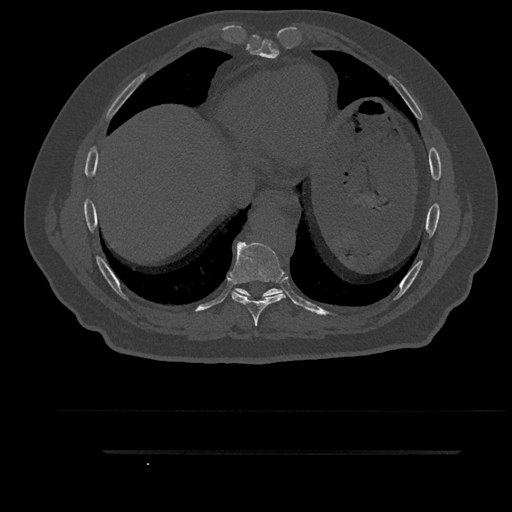
CT including the spine, one axial slice; slice 459 of 797 in the series (ordered by position); bone window (W 1800 / L 400 HU); 0.5 mm slice thickness; 512 × 512 image matrix, field of view 432 × 432 mm. Male patient, age 63 years. From the clinical record (not read from this slice): primary cancer: renal.
Annotated regions visible in this slice (semi-automatically segmented with operator editing):
- T8 vertebra: bounding box (x1, y1, x2, y2) in pixels: (231, 242, 285, 326)
- T9 vertebra: (234, 288, 283, 299)